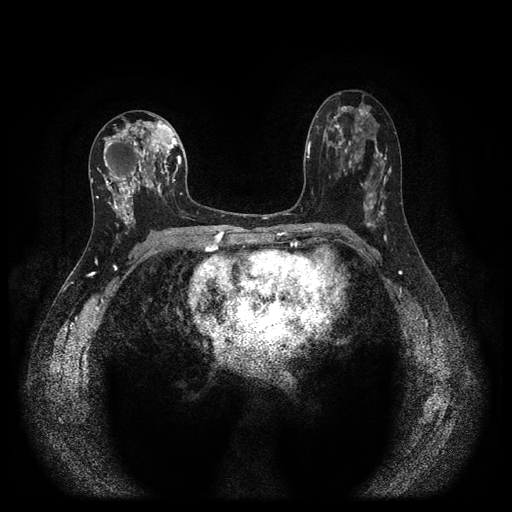
Breast MRI (dynamic contrast-enhanced, multi-phase), one axial slice. Slice 55 of 116 in the series (ordered by position). Dynamic contrast-enhanced series, time point 2 of 5 at this slice position (early post-contrast). 1.5 T. TE 2.7 ms, TR 5.4 ms. 512 × 512 image matrix. Patient: female, 47 years.
Annotated regions visible in this slice (semi-automatically segmented with operator editing):
- breast lesion (labelled 'tumour' in the annotation; benign lesions carry a separate 'benign' label): bounding box (x1, y1, x2, y2) in pixels: (97, 117, 176, 234)